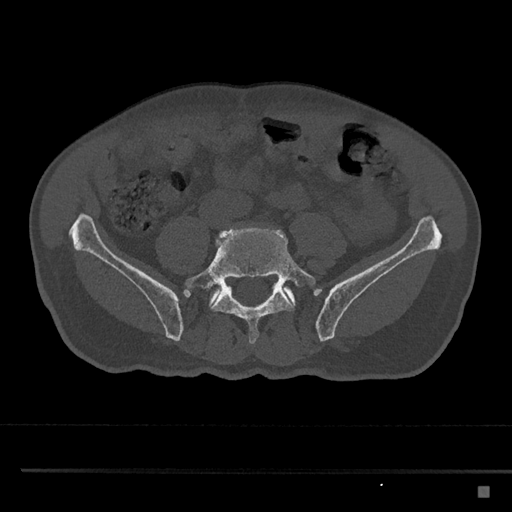
CT including the spine, one axial slice; position 578 of 797 along the scan axis; bone window (W 1800 / L 400 HU); 0.5 mm slice thickness; 512 × 512 image matrix, field of view 391 × 391 mm. Patient: male, 59 years. From the clinical record (not read from this slice): primary cancer: prostate.
Annotated regions visible in this slice (semi-automatic segmentation, software-assisted and operator-edited):
- L5 vertebra: bounding box (x1, y1, x2, y2) in pixels: (183, 226, 316, 345)